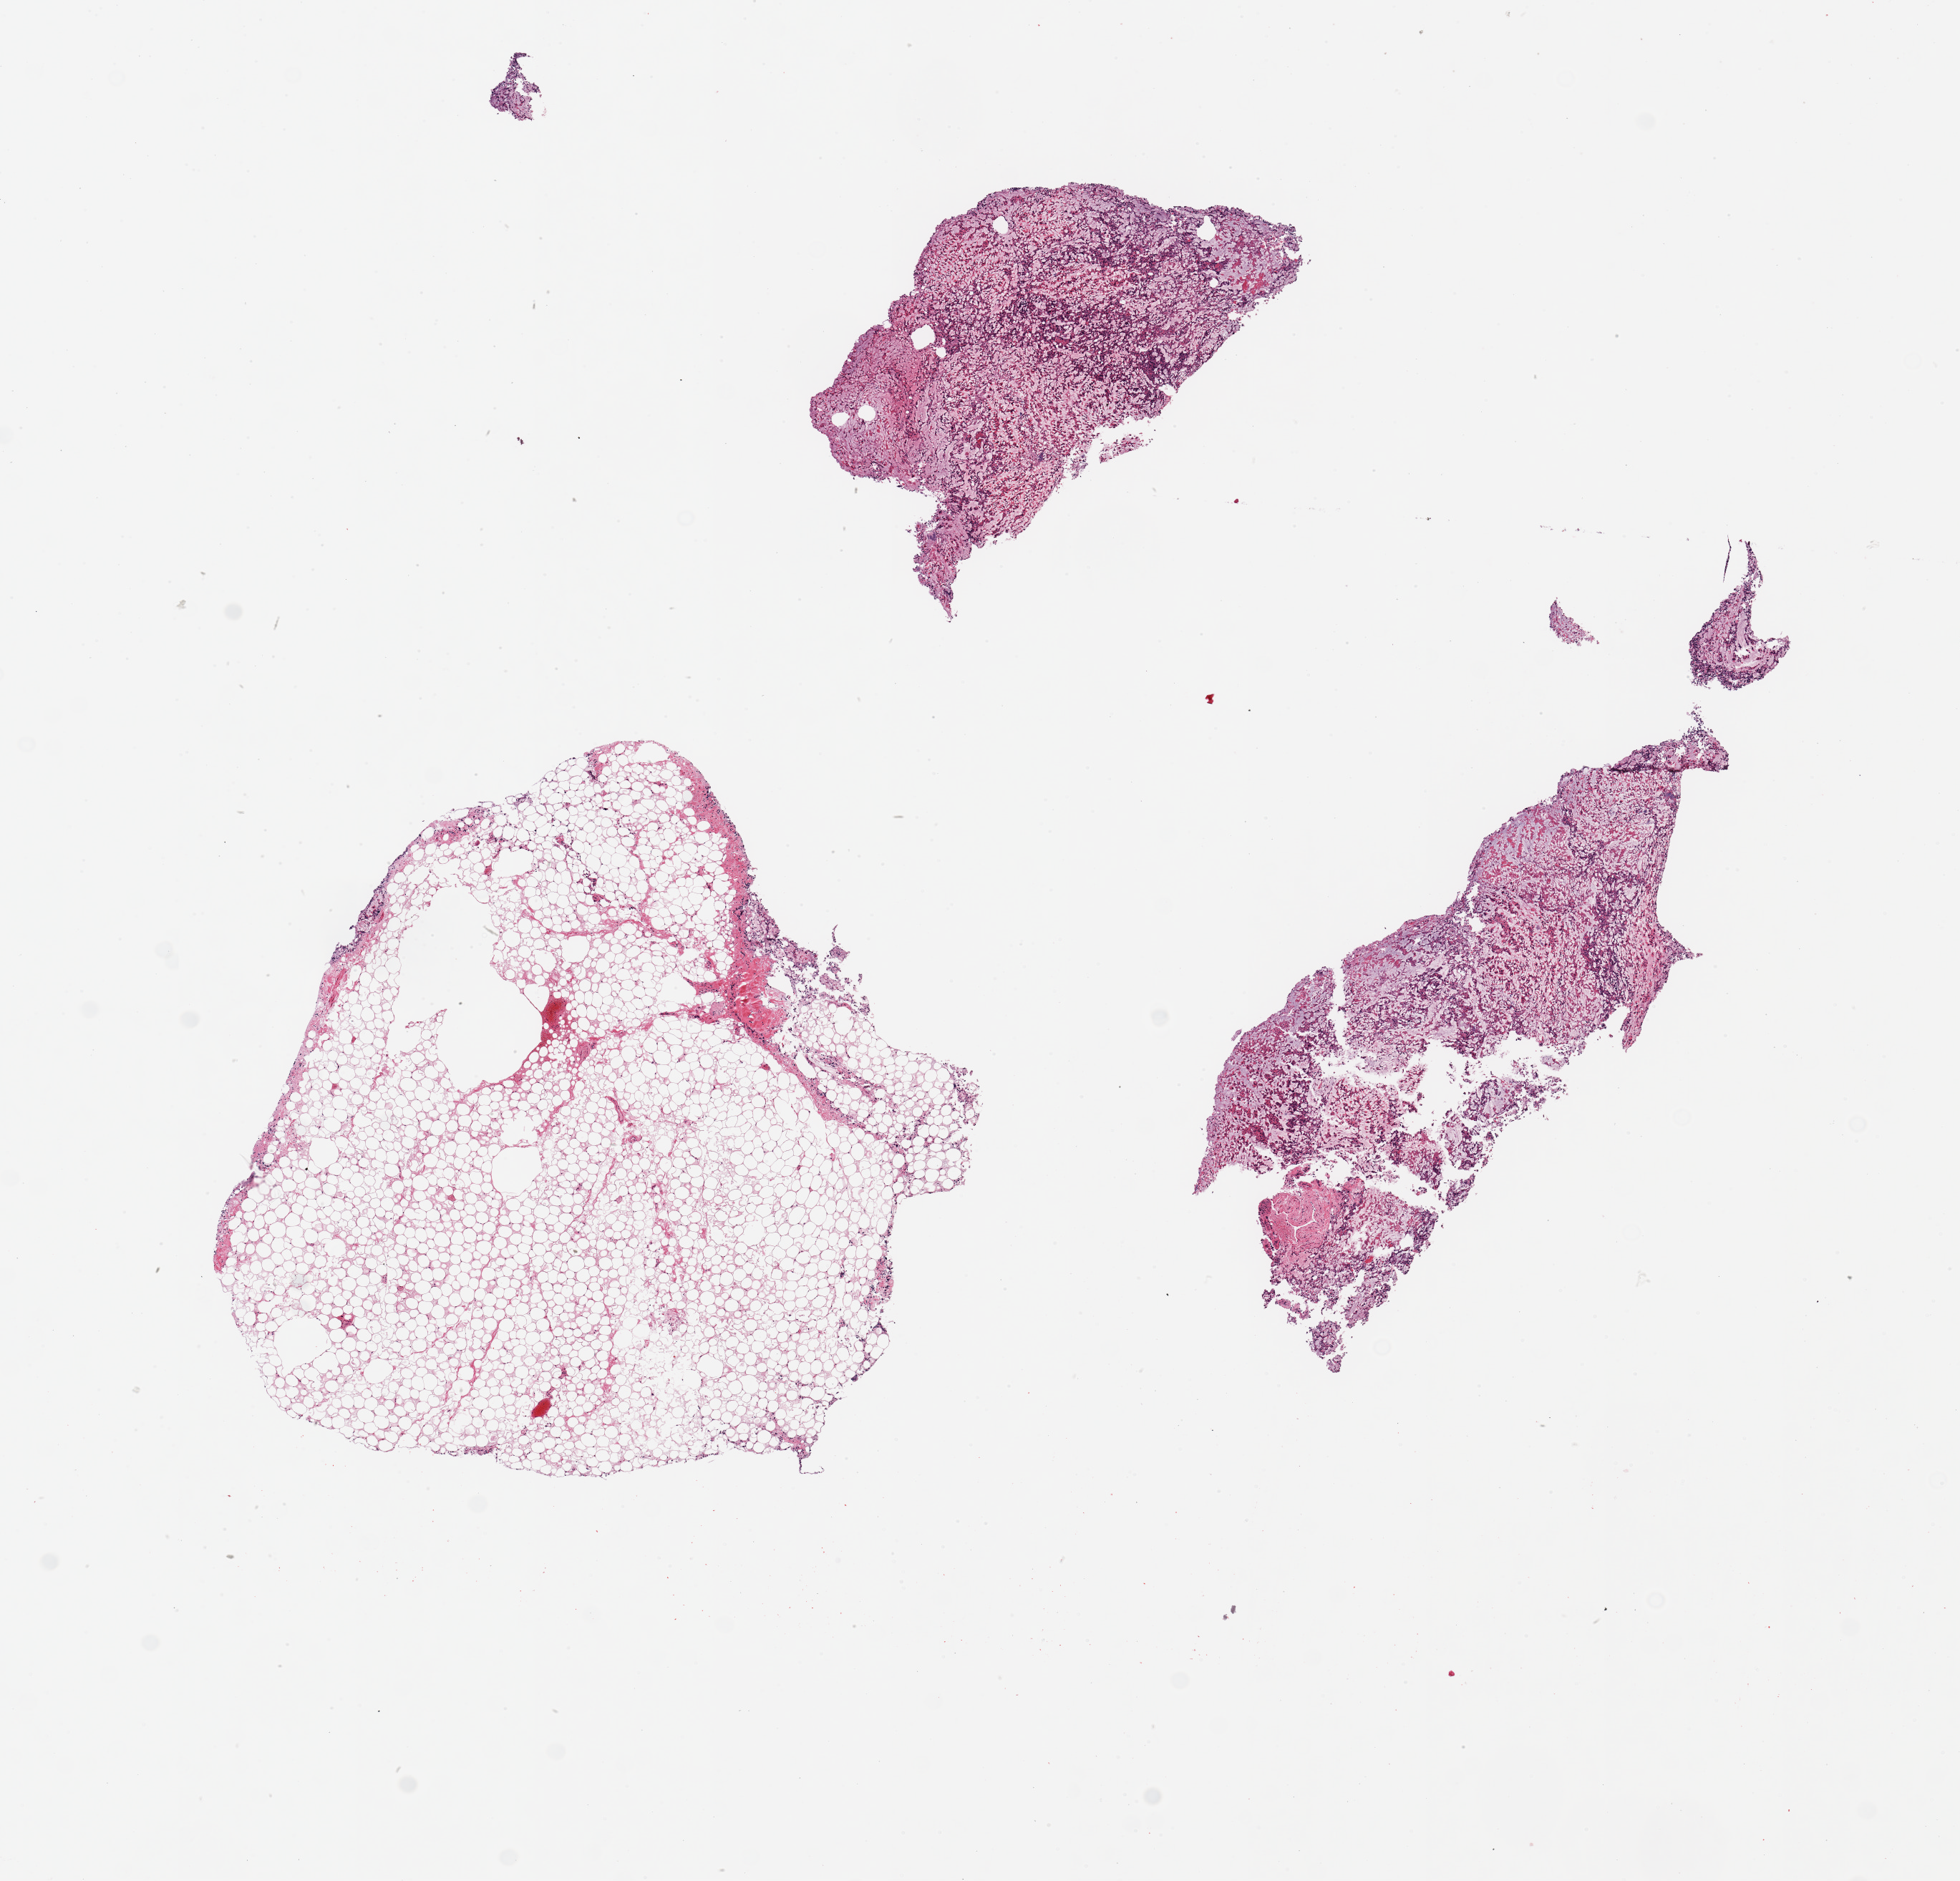
Digitized haematoxylin and eosin-stained section, brightfield, whole scanned area (about 10.8 x 10.4 mm, from a 20x scan) shown as a low-resolution overview. PAXgene-fixed, paraffin-embedded tissue. Section of ileum (target tissue). Tissue donor sample. Donor: female.
• pathologist's review note for this sample: 2 pieces ~2x2mm, all autolyzed mucosa, no lymphoid elements. One aggregate of fat